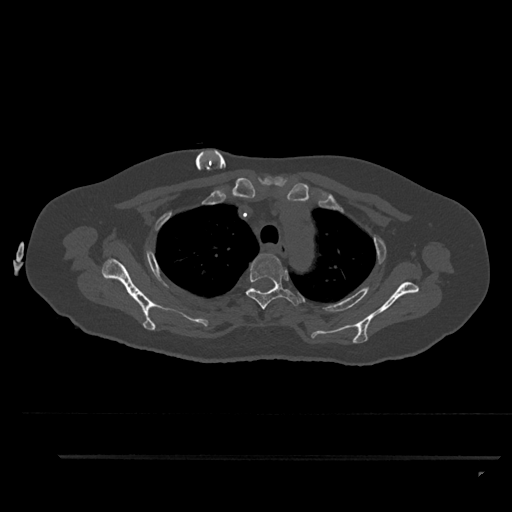
CT including the spine, one axial slice; slice 685 of 797 in the series (ordered by position); reconstruction kernel Br40s/3; 120 kVp; bone window (W 1800 / L 400 HU); 0.5 mm slice thickness; 512 × 512 image matrix. Female patient, age 44 years. From the clinical record (not read from this slice): primary cancer: renal; vertebrae with lytic lesions (as recorded): L1.
Annotated regions visible in this slice (semi-automatically segmented with operator editing):
- T3 vertebra: box from (x=245, y=254) to (x=300, y=309) px